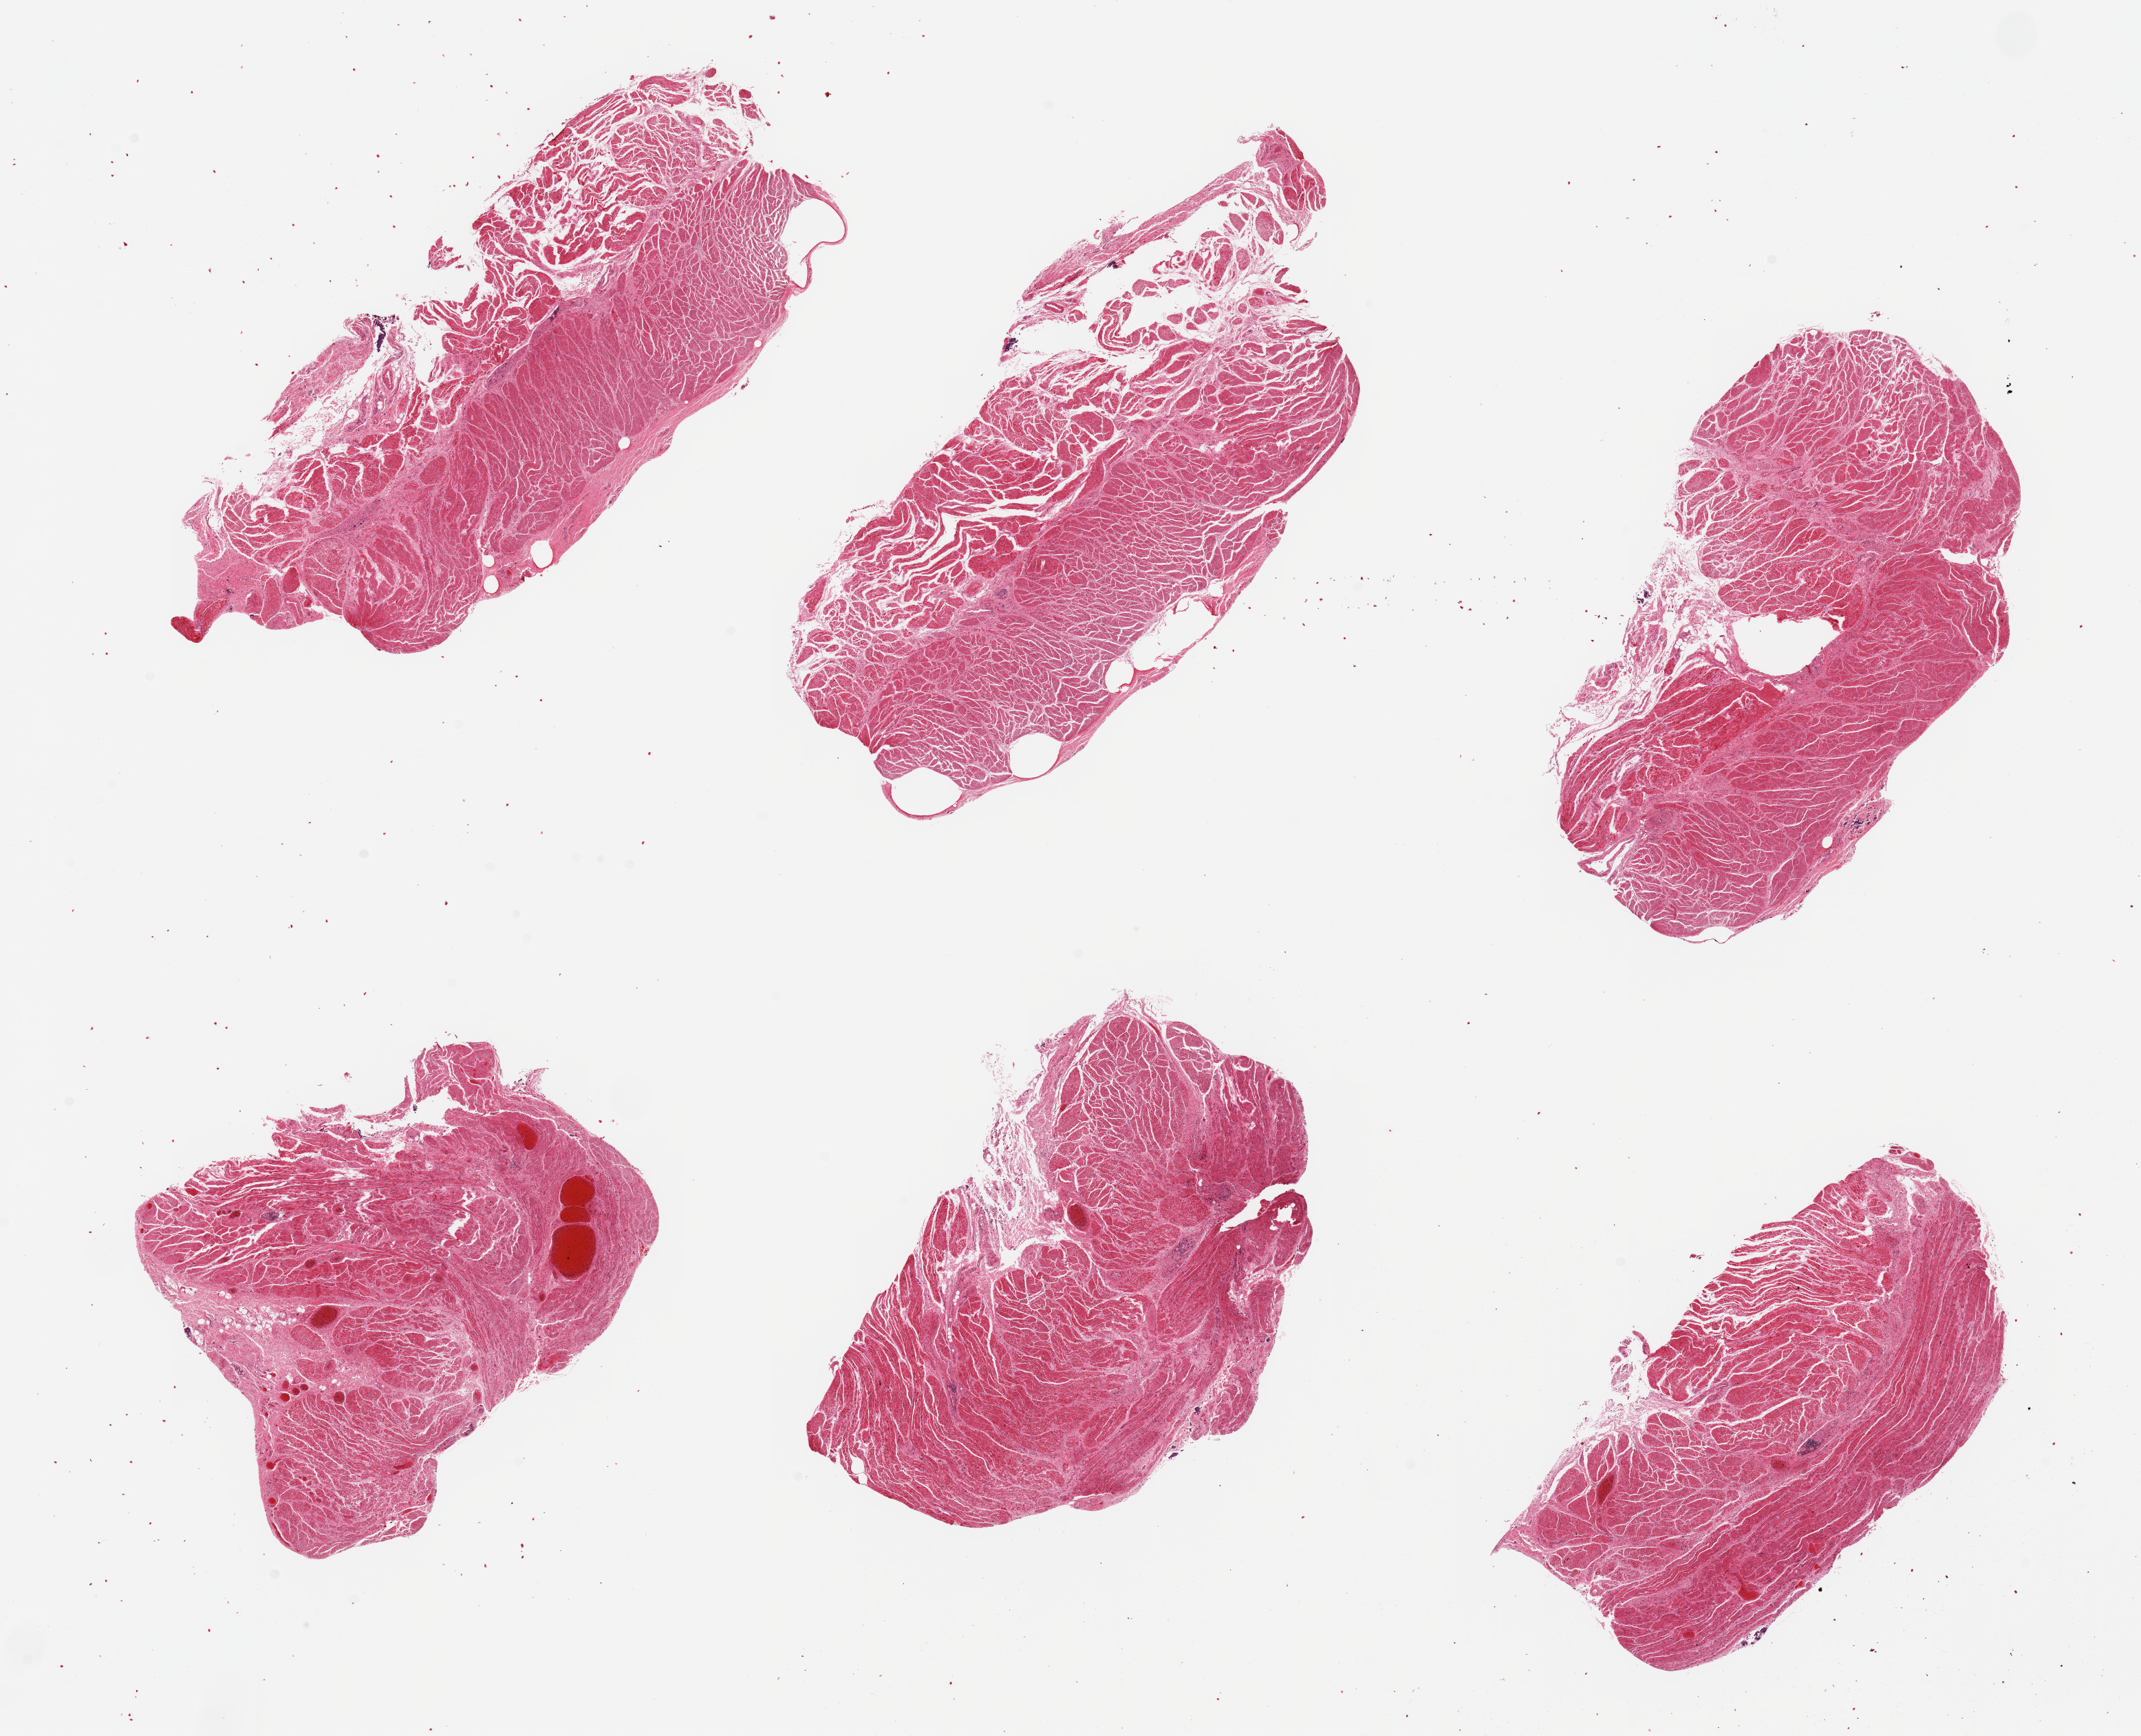
Digitized haematoxylin and eosin-stained section, a low-resolution overview of the entire scanned area, about 24.6 x 20.0 mm (slide scanned at 20x). PAXgene-fixed, paraffin-embedded tissue. Section of gastroesophageal junction (target tissue). Donor tissue sample. Donor: male.
Pathologist's review note for this sample: 6 pieces, all muscularis.